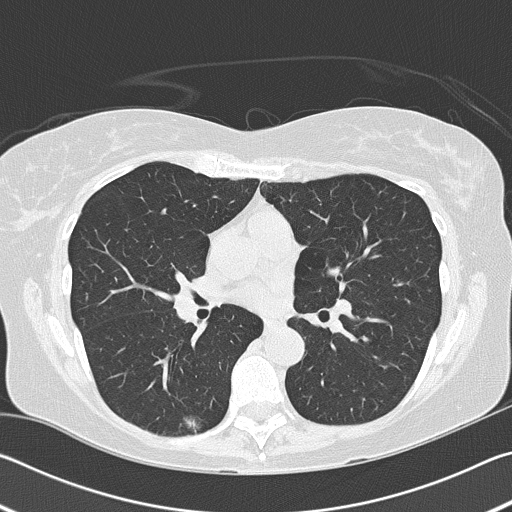
Chest CT (low-dose screening protocol), one axial image; baseline screening round; lung window (W 1500 / L -600 HU); 120 kVp; slice 75 of 159 in the series; 512 × 512 image matrix. Female, age 60 years at enrolment. Former smoker at enrolment.
Expert reader's lesion annotation, bounding box [x1, y1, x2, y2] px = [171, 407, 216, 443]. The screening reader recorded 2 non-calcified nodules or masses ≥4 mm on this exam (right lower lobe, right middle lobe); which of them this box marks is not recorded. Official screen result: positive, change unspecified: nodule(s) >= 4 mm or enlarging nodule(s), mass(es), or other non-specific abnormalities suspicious for lung cancer. Lung cancer was diagnosed 799 days after this screen: acinar cell carcinoma, right lower lobe, moderately differentiated (G2), stage IA (AJCC 6th edition), 10 mm at pathology.